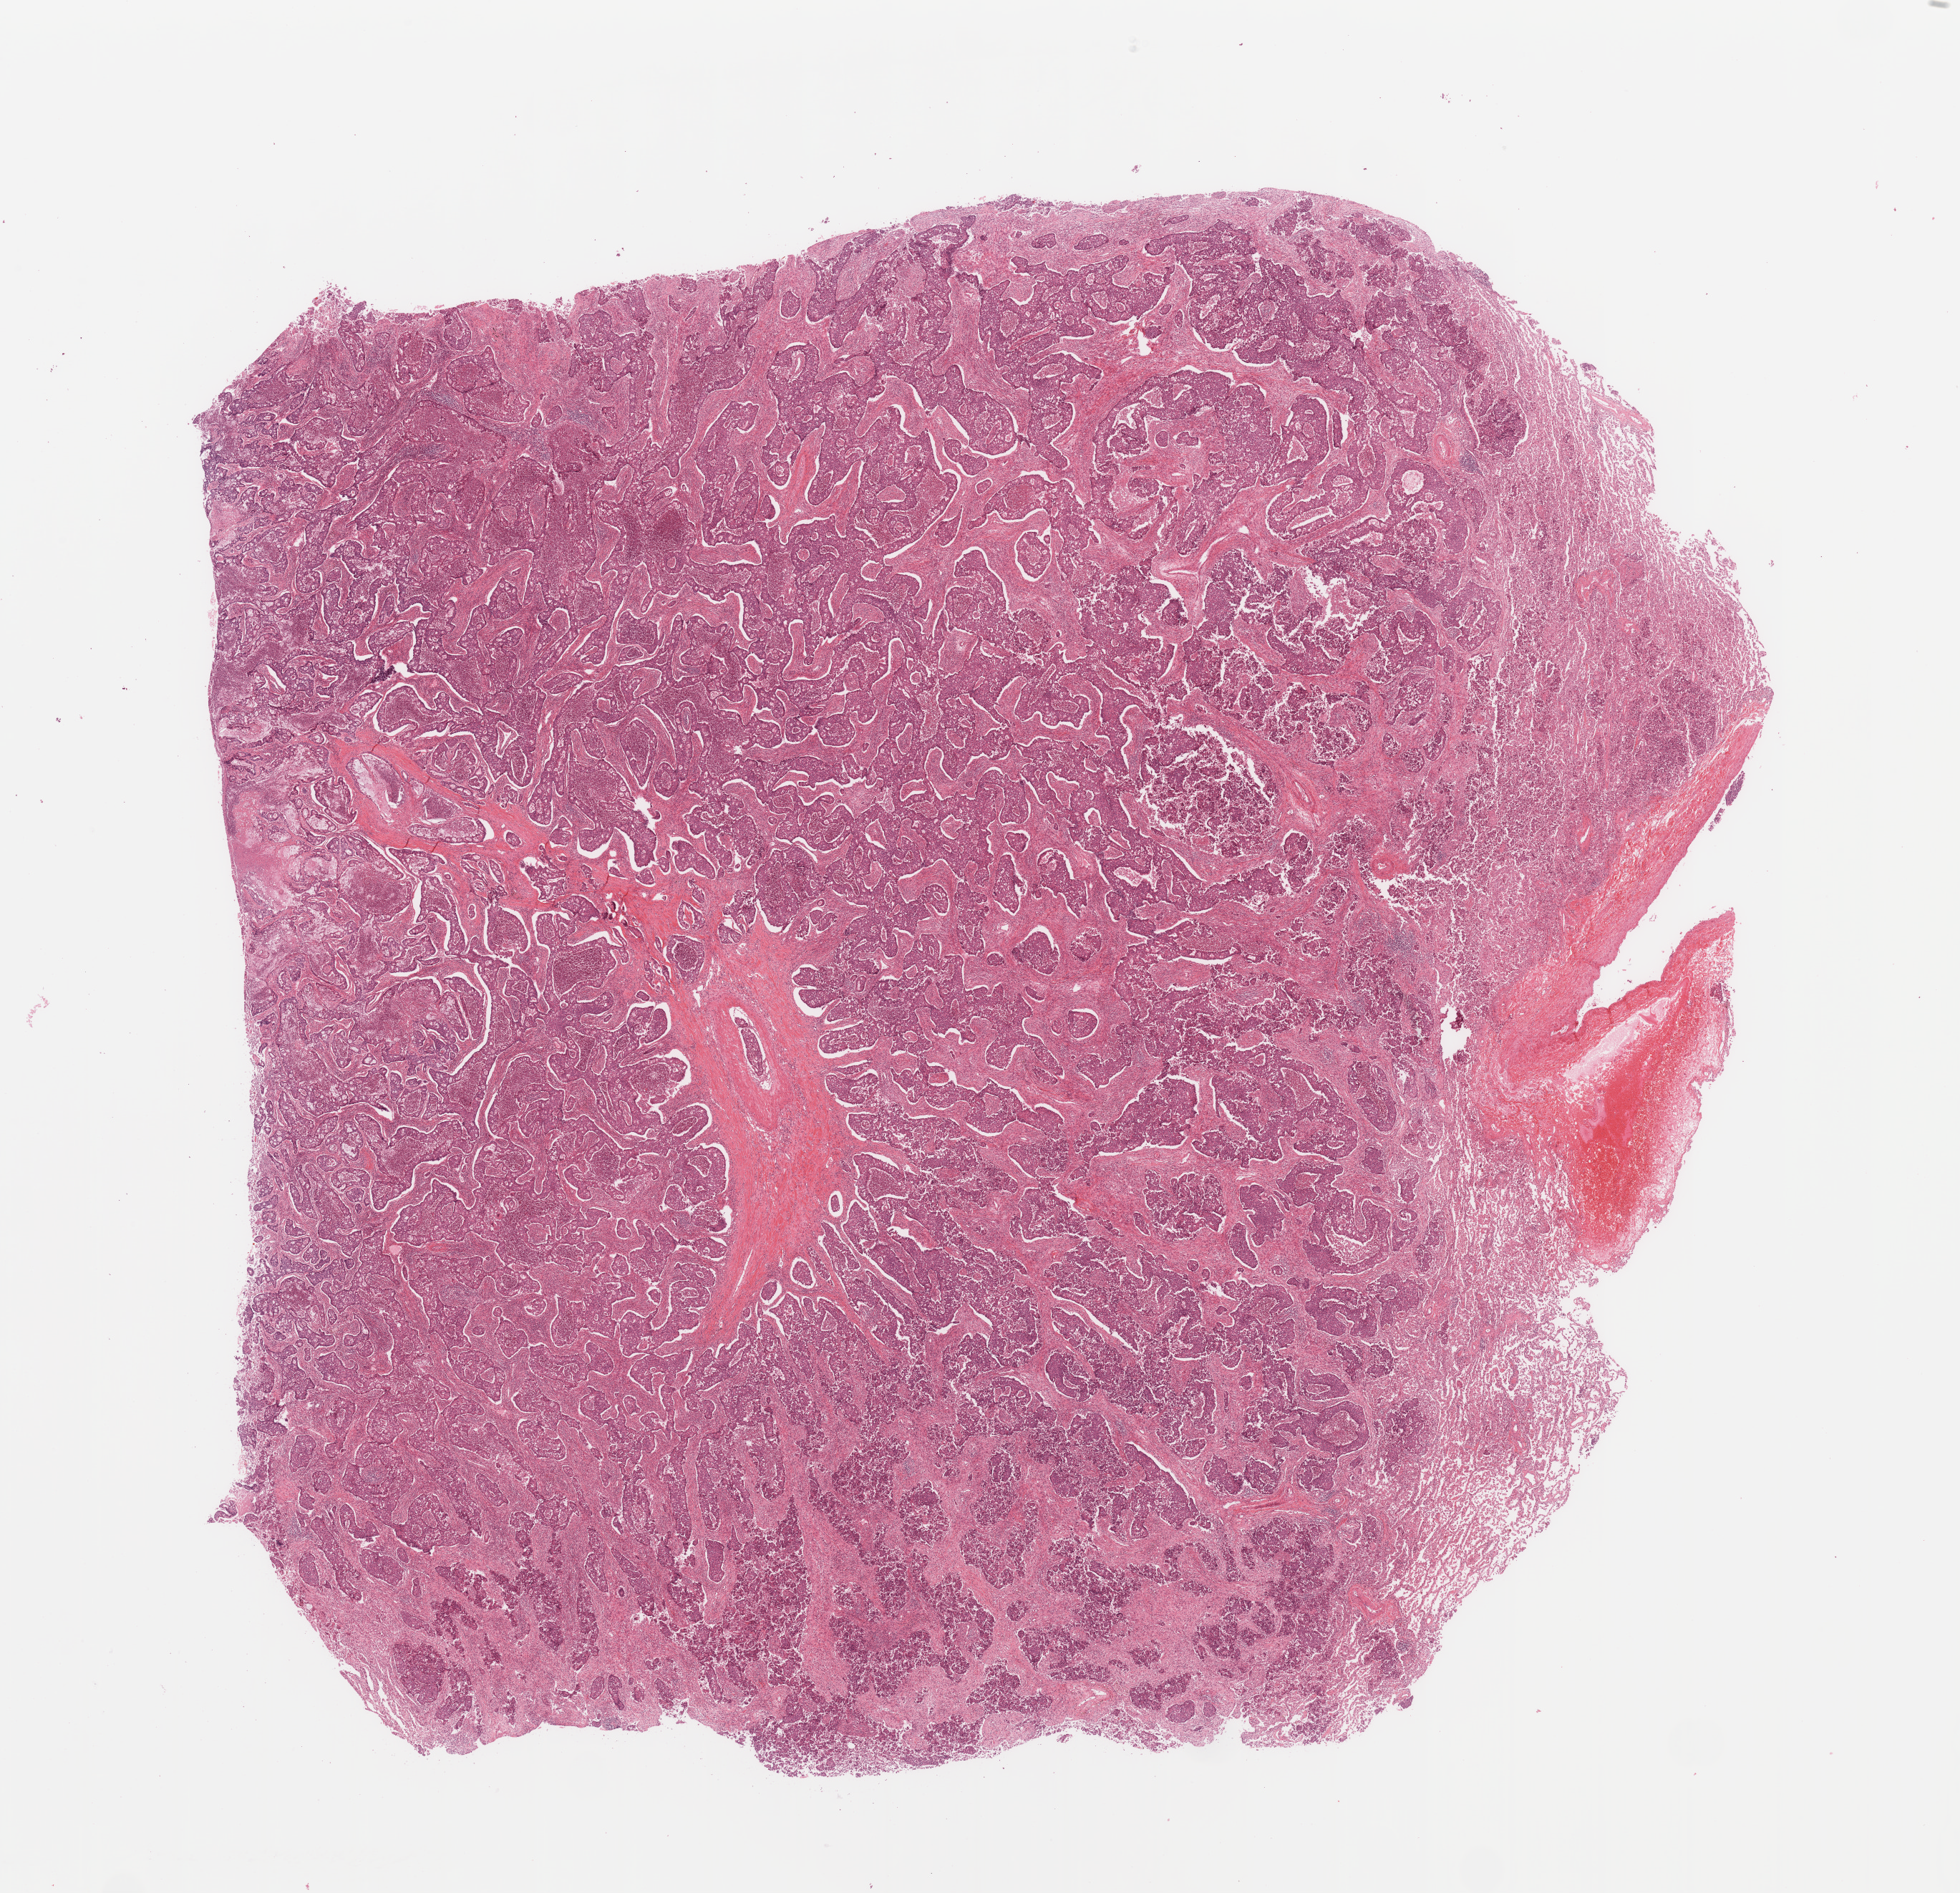
H&E whole-slide image — low-resolution overview of the scanned area, about 21.7 x 20.9 mm; tumour tissue sample, sampled site: lung. Male, 58 y/o. Histologic grade: G3 (poorly differentiated). Composition of this section per pathologist review: tumour nuclei 70%, necrosis 10%.
- diagnosis: Adenocarcinoma, NOS
- AJCC pathologic stage: IIIA